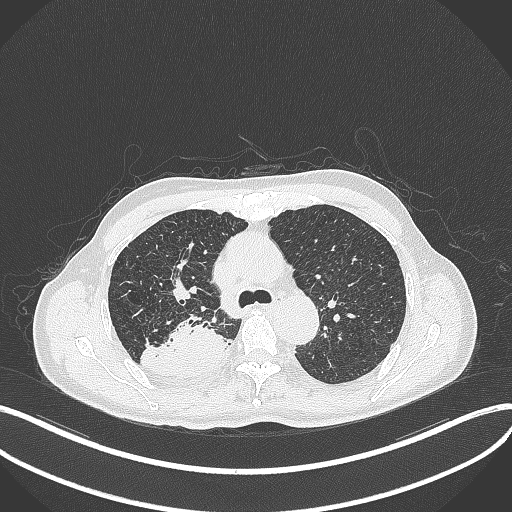
Chest CT, one axial slice; slice 313 of 428 in the series (ordered by position); reconstruction kernel B70f; lung window (W 1500 / L -600 HU); 1 mm slice thickness; 512 × 512 image matrix. Male patient, age 79 years. Case-level facts recorded for this patient, not image findings: clinical TNM (as recorded): T3 N0 M0.
Outlined on this slice (bounding box drawn by a radiologist):
- lung tumour (recorded histology: adenocarcinoma): bounding box <138,312,228,380> (left, top, right, bottom; pixels)